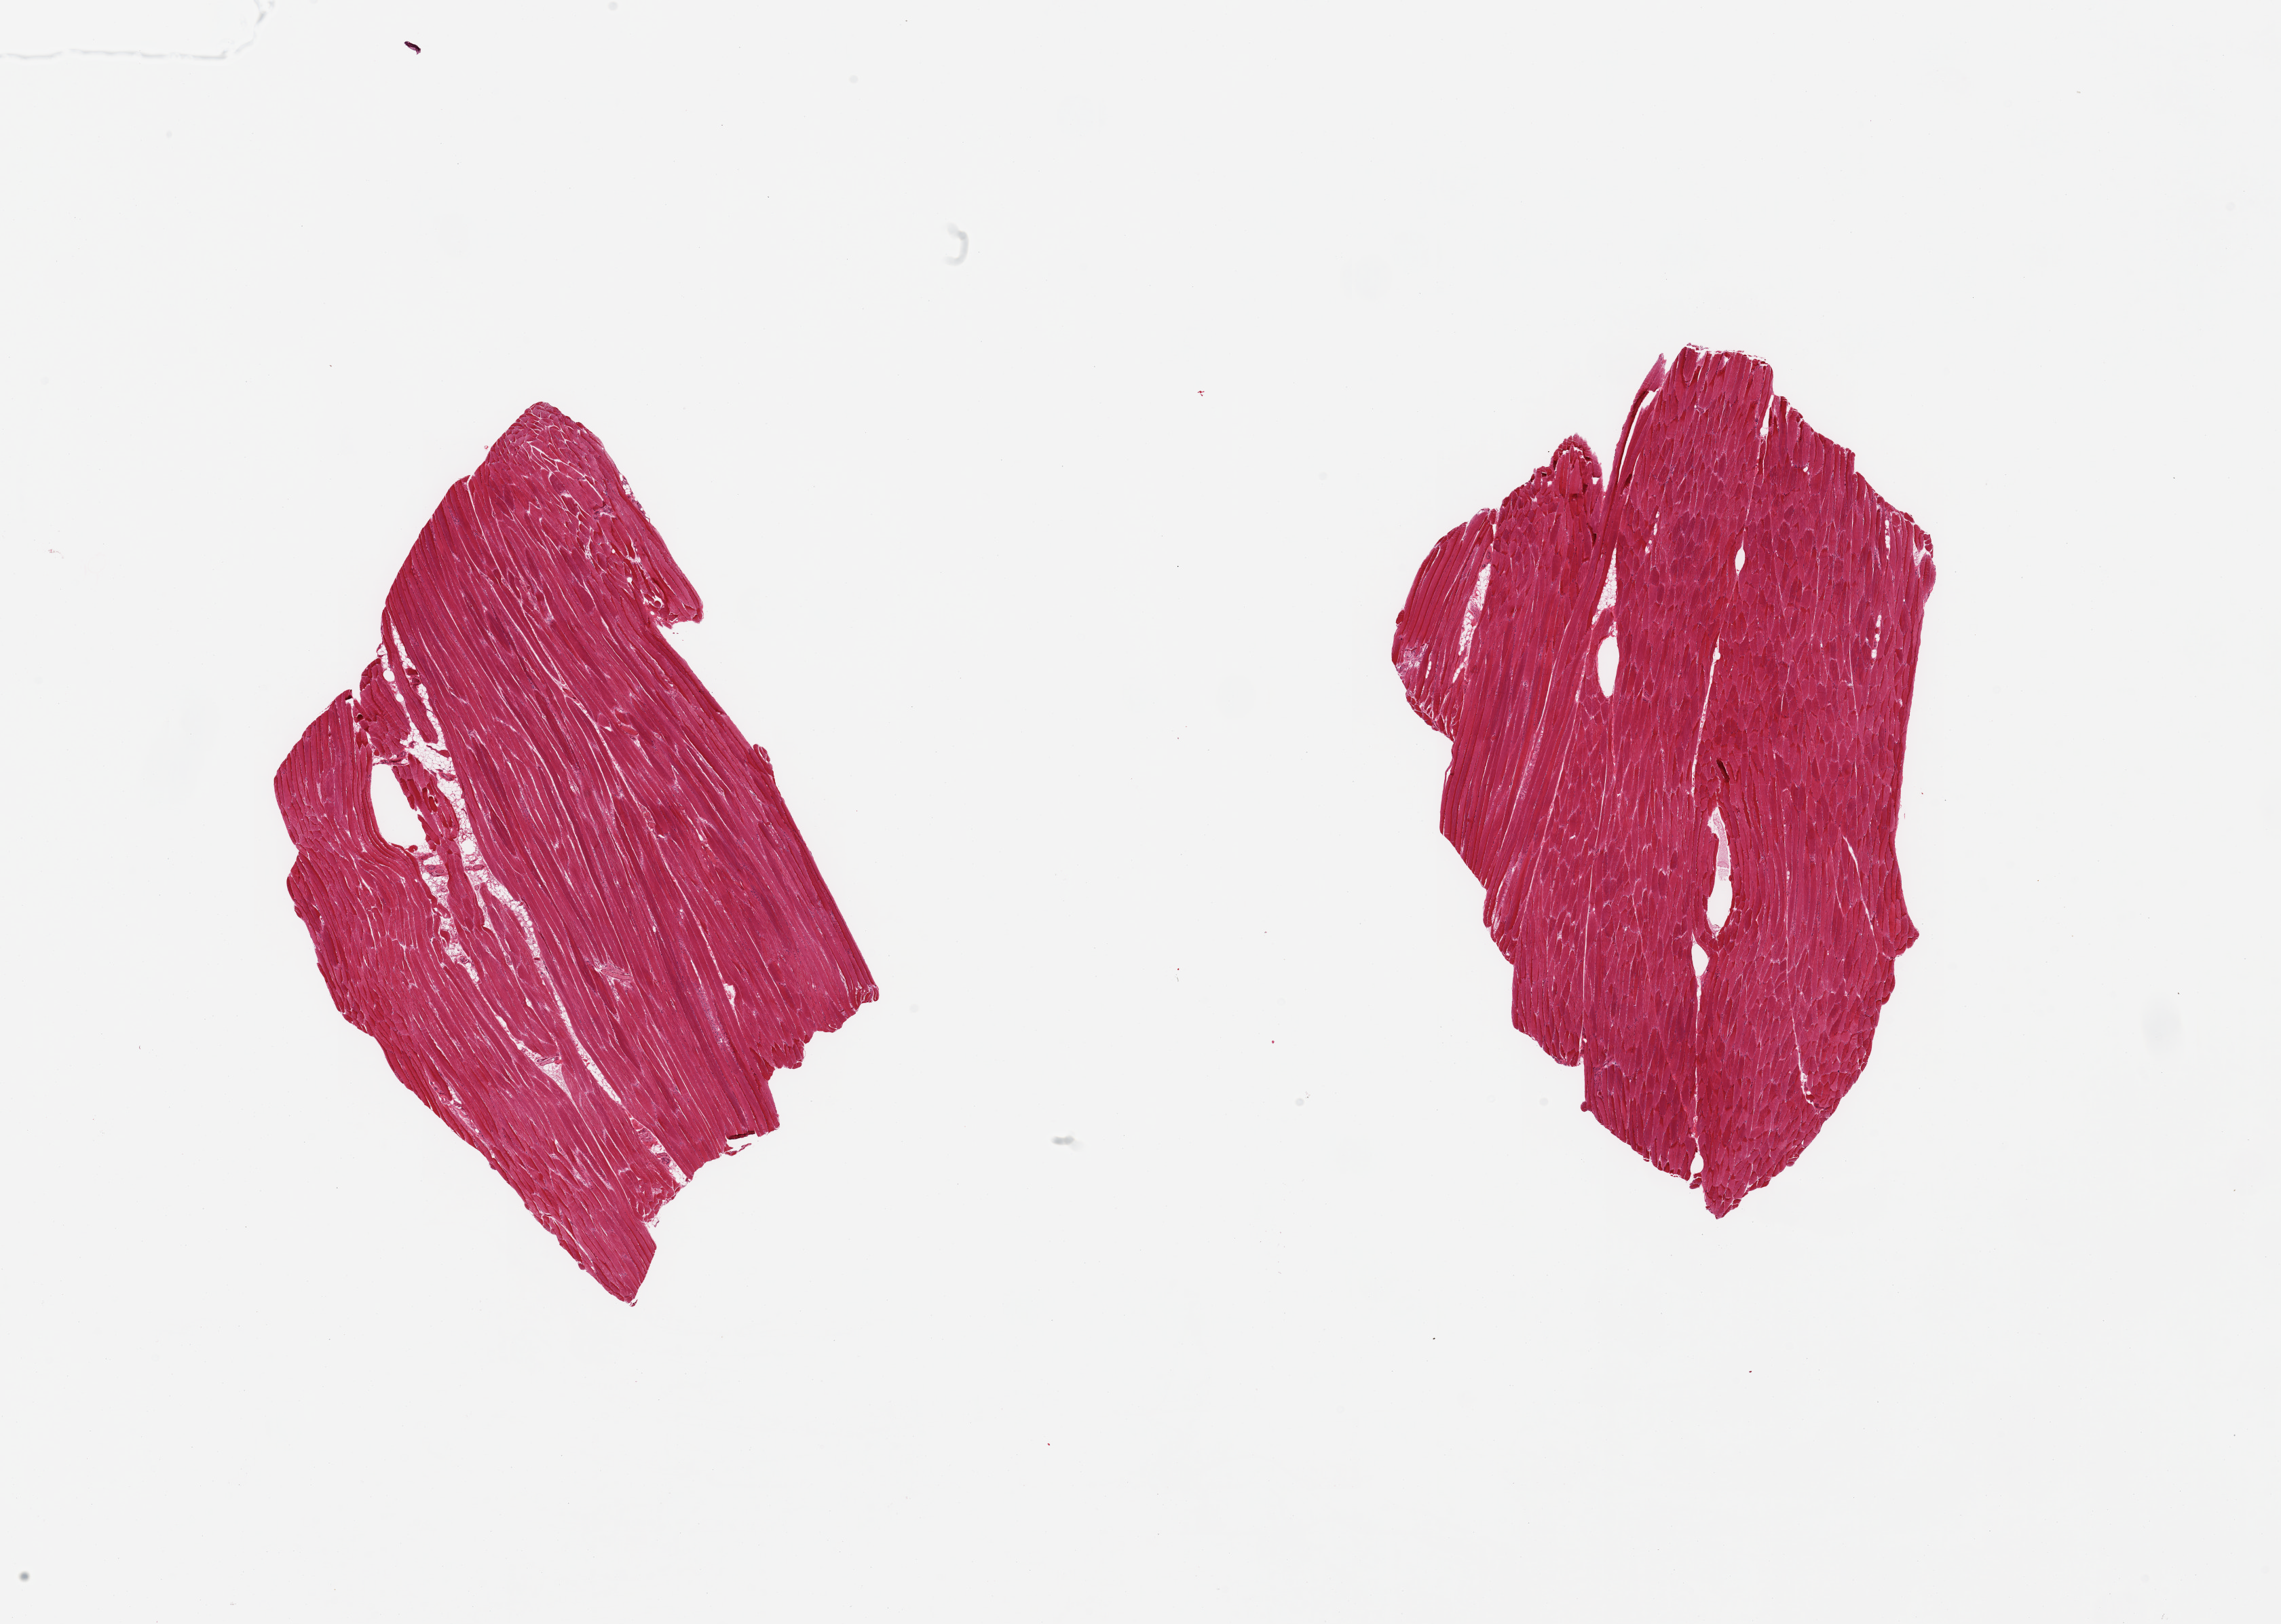
H&E whole-slide image — shown as a low-resolution overview of the whole scanned area (about 26.6 x 18.9 mm); PAXgene-fixed paraffin-embedded (PFPE) section; sampled site (target tissue): skeletal muscle; tissue donor sample. Male donor.
- review note (as recorded): 2 pieces